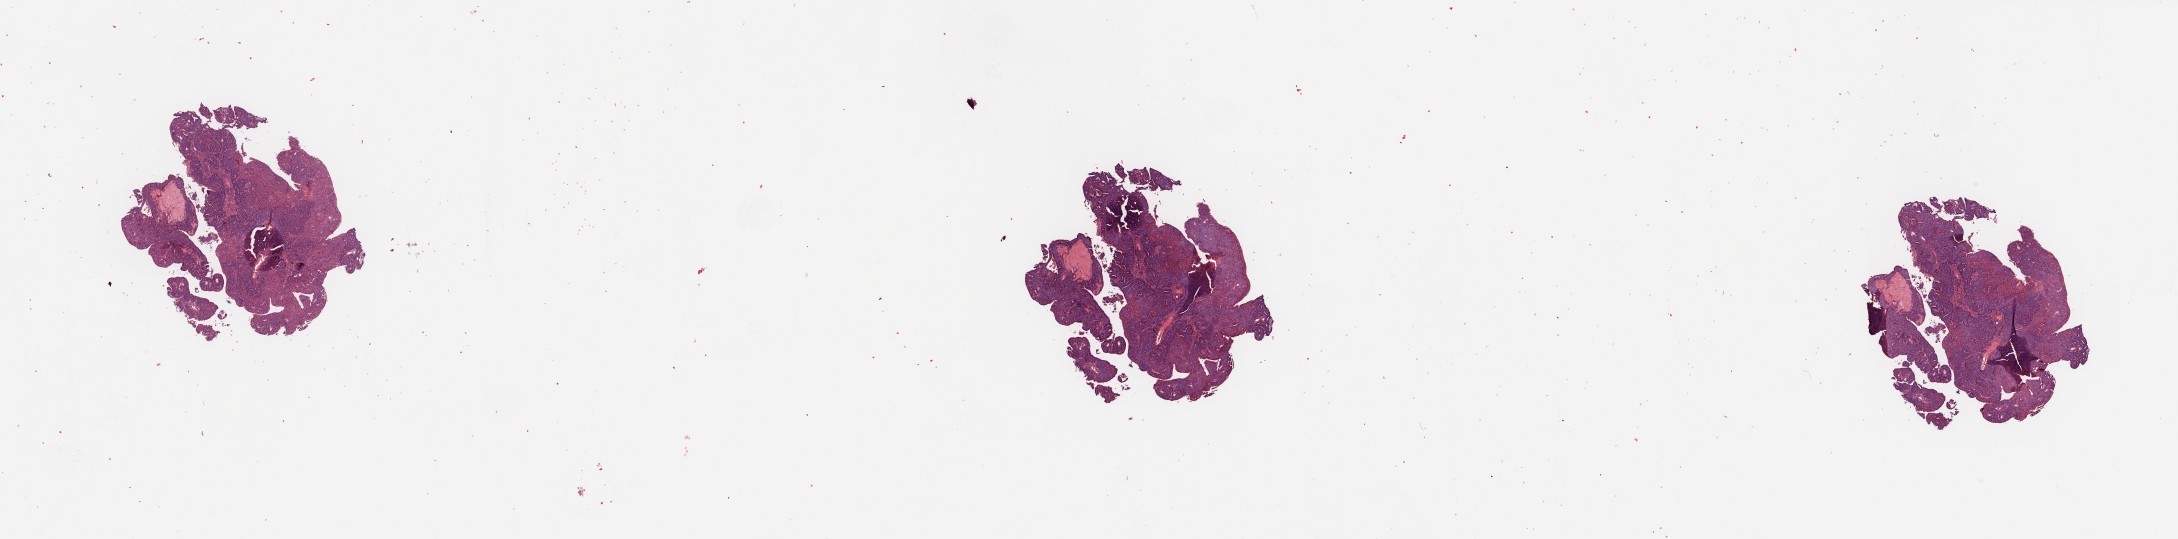
Whole-slide histology image, Hematoxylin and eosin (H&E) stained — shown as a low-resolution overview of the whole scanned area (about 34.5 x 8.5 mm, slide scanned at 20x); tumour tissue sample, sampled site: uterus. 69-year-old female patient. Histologic grade: G3 (poorly differentiated). Pathologist review of this section (percent, as recorded): tumour nuclei 90%, necrosis 5%.
• histologic diagnosis: Endometrioid adenocarcinoma, NOS
• primary tumour site (as recorded): anterior endometrium
• AJCC pathologic stage: I